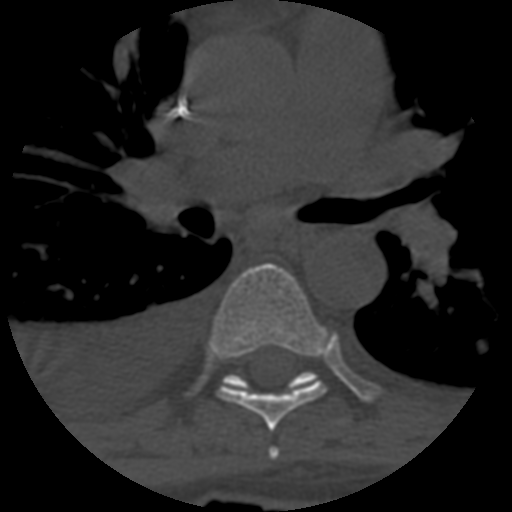
CT including the spine, one axial slice. Position 431 of 708 along the scan axis. Reconstruction kernel STANDARD. One of 3 acquisitions stored at this slice position. Bone window (W 1800 / L 400 HU). 1.25 mm slice thickness. 512 × 512 image matrix, field of view 160 × 160 mm. Patient age 55 years. Case-level facts recorded for this patient, not image findings: primary cancer: colon; vertebrae with lytic lesions (as recorded): T12, L1, L5.
Annotated regions visible in this slice (semi-automatic segmentation, software-assisted and operator-edited):
- T5 vertebra: bounding box <268,447,280,460> (left, top, right, bottom; pixels)
- T6 vertebra: <211,263,325,432>
- T7 vertebra: <223,372,315,387>